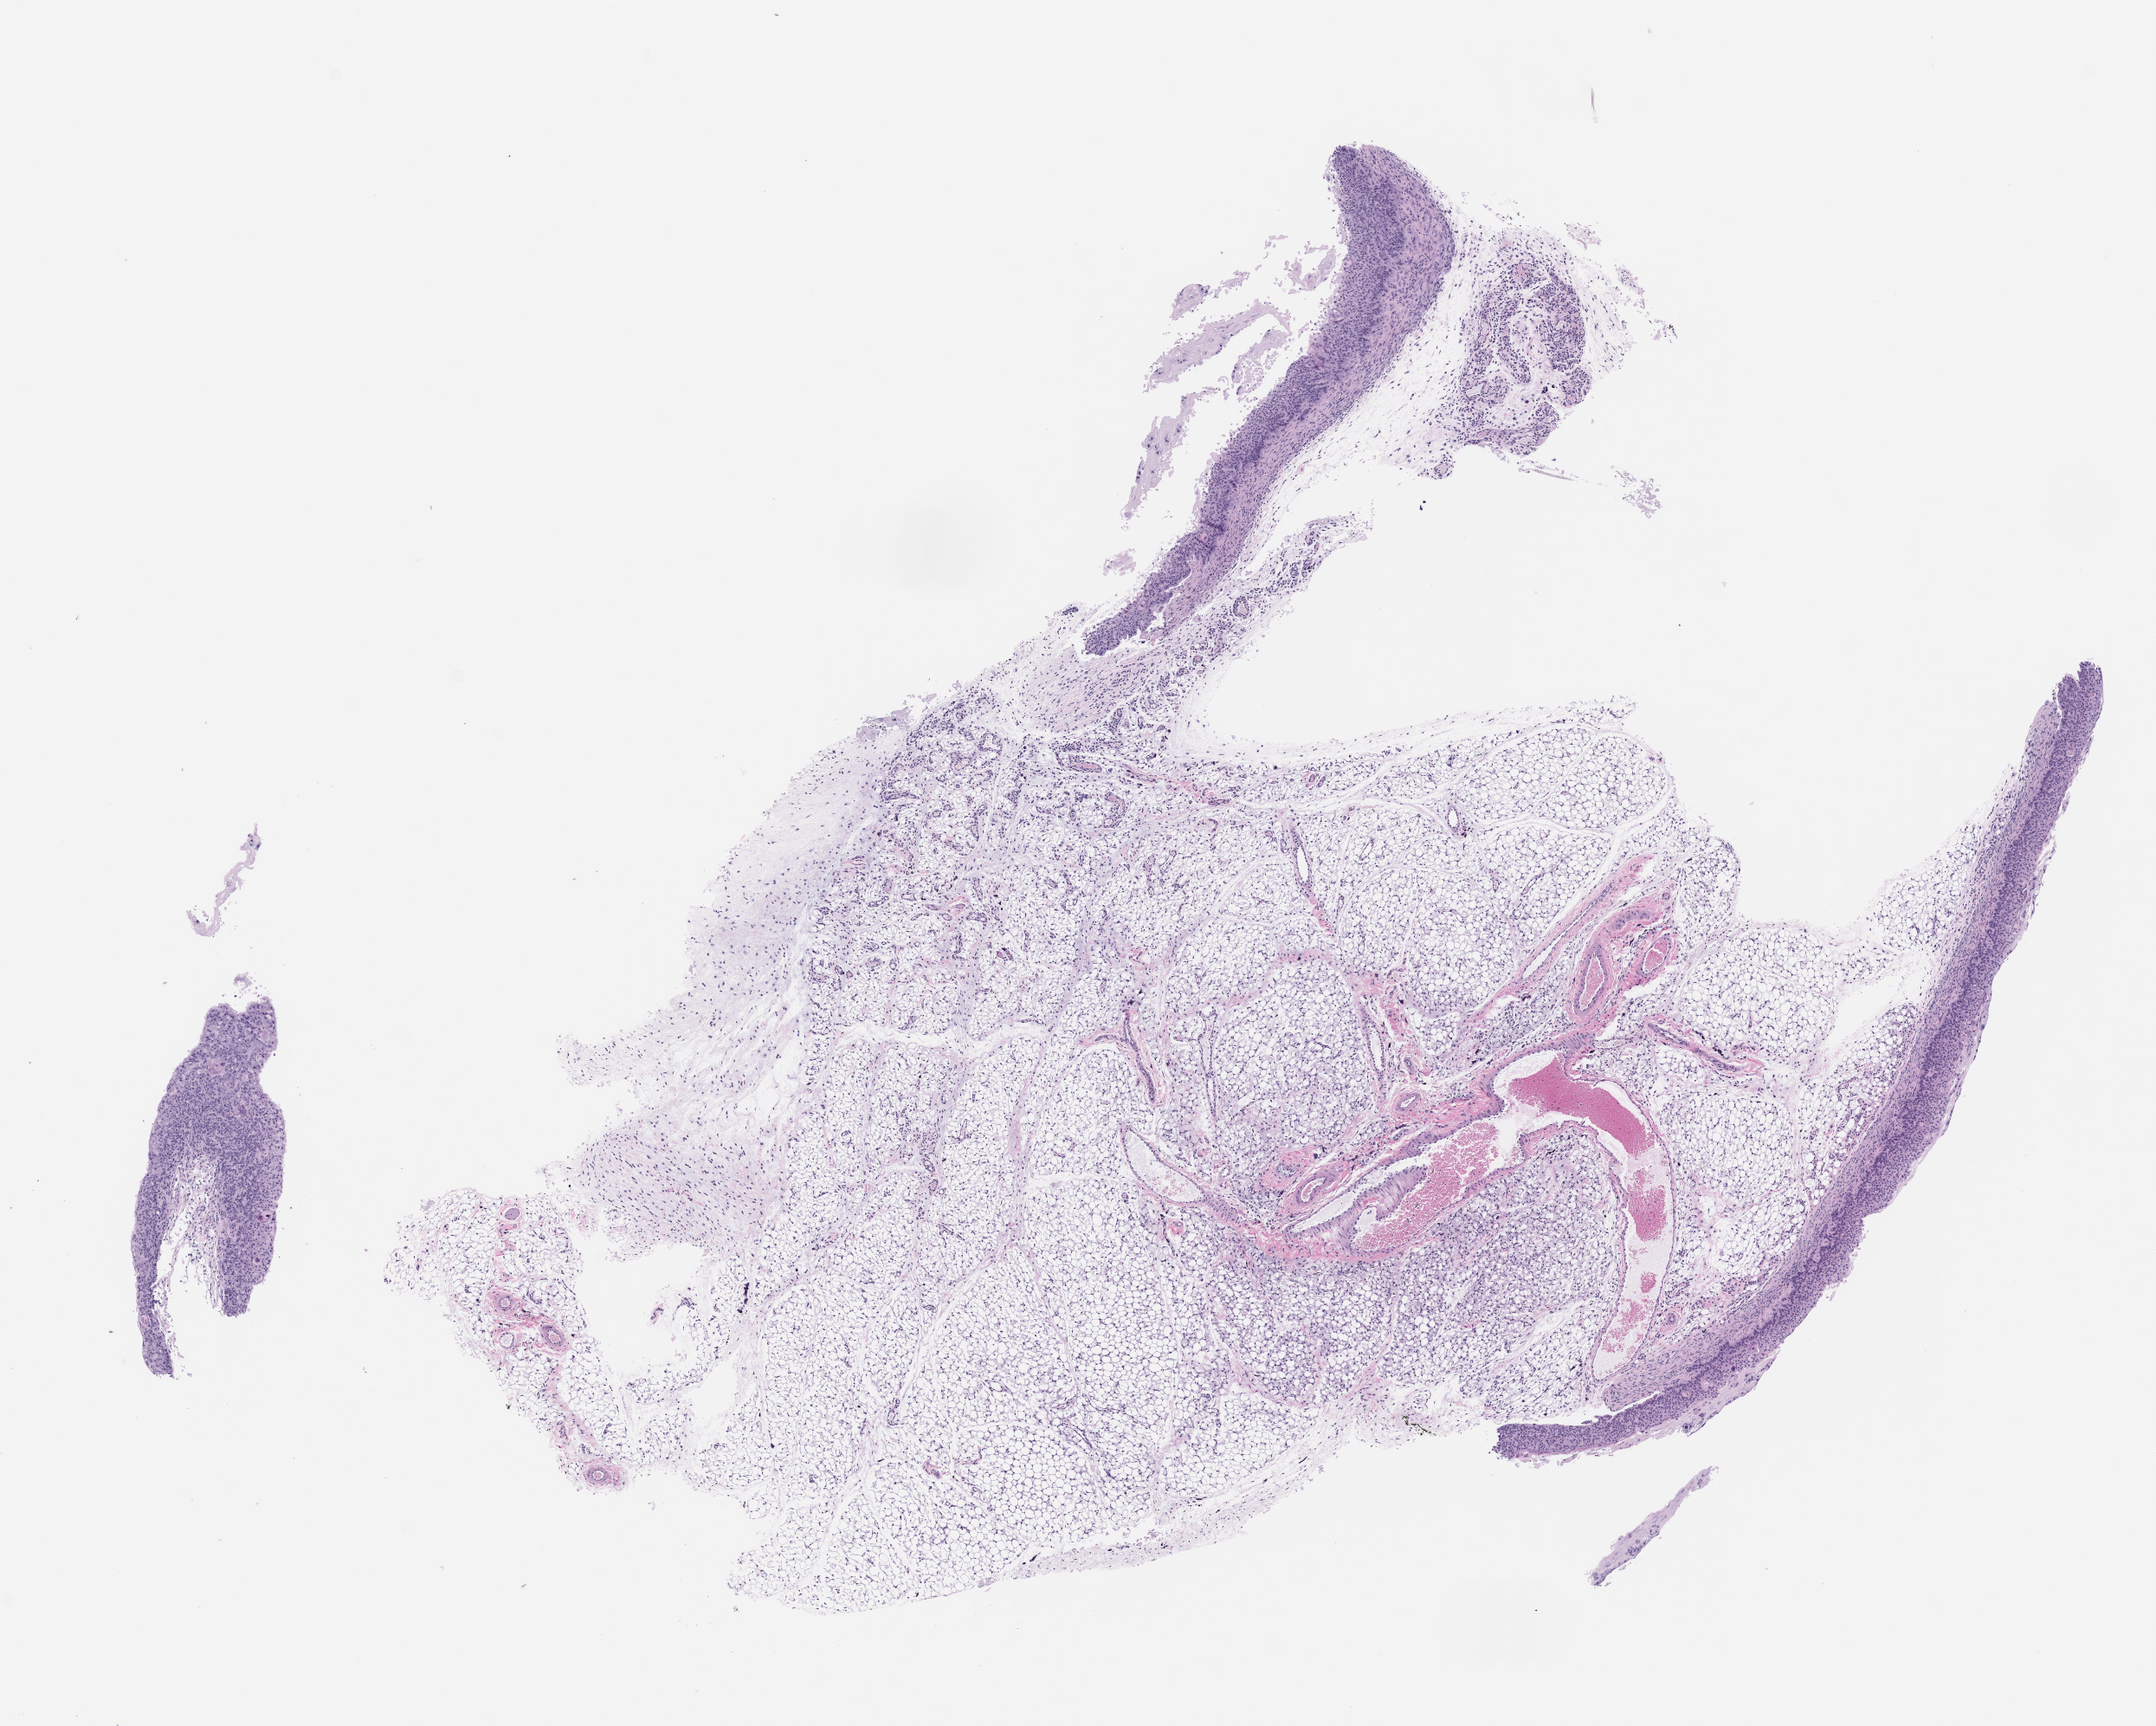
Hematoxylin and eosin (H&E) whole-slide image of a patient-derived xenograft (PDX) tumor grown in a mouse, low-resolution overview of the scanned area, about 10.0 x 8.0 mm, FFPE section, tumor site category: larynx.
Originating patient diagnosis: Head and Neck Squamous Cell Carcinoma.